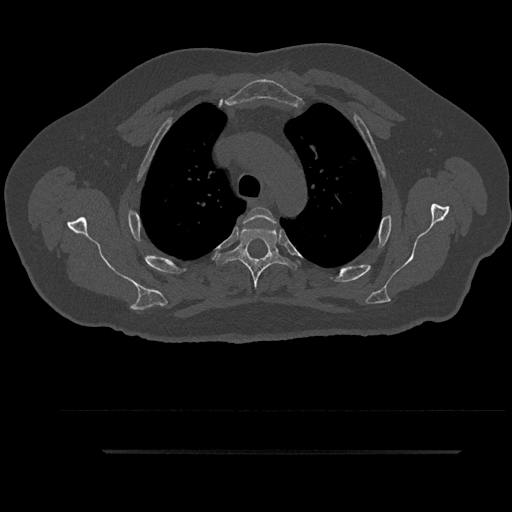
CT including the spine, one axial slice; slice 680 of 797 in the series (ordered by position); 120 kVp; bone window (W 1800 / L 400 HU); 0.5 mm slice thickness; 512 × 512 image matrix, field of view 432 × 432 mm. Patient: male, 63 years. Case-level facts recorded for this patient, not image findings: primary cancer: renal.
Outlined on this slice (semi-automatic segmentation, software-assisted and operator-edited):
- T3 vertebra: bounding box <244,207,276,224> (left, top, right, bottom; pixels)
- T4 vertebra: <215,227,298,298>